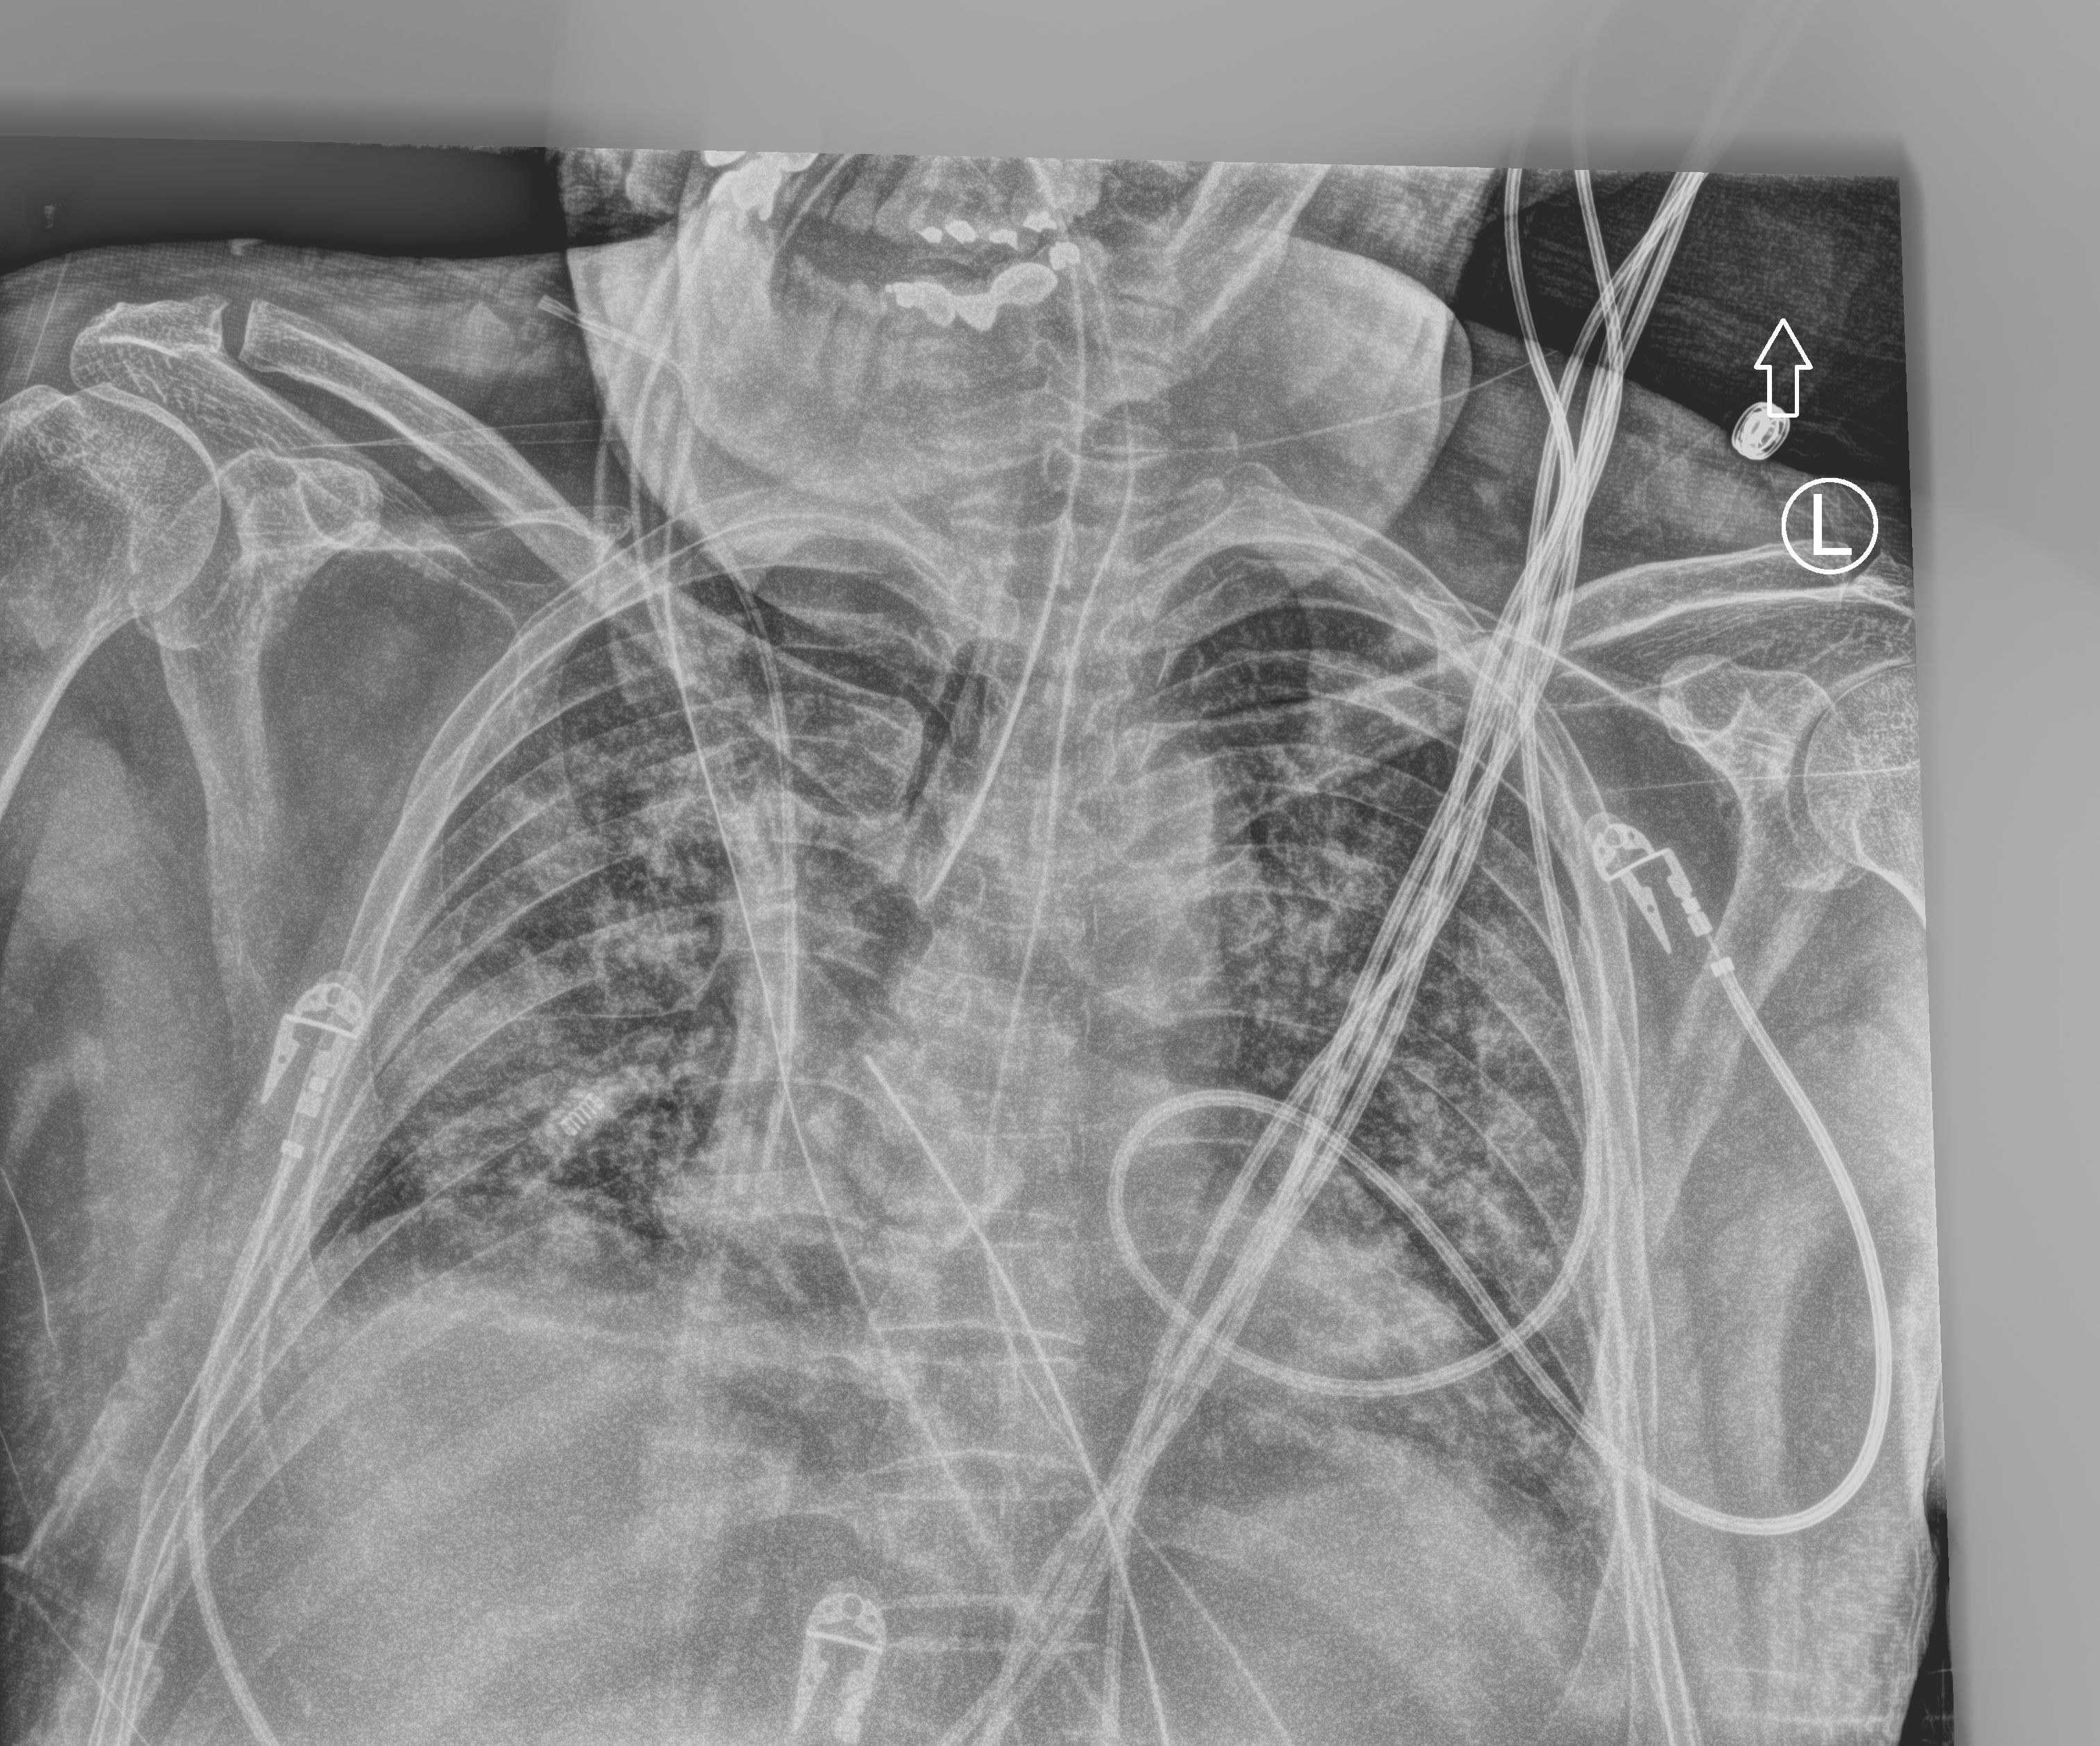
Bedside chest radiograph (computed radiography), anteroposterior (AP) projection. Patient hospitalised with COVID-19; male, aged 60–74 years.
Hospital-stay facts (about this admission, not read from this image; timing relative to this image not recorded): admitted to intensive care during this hospital stay: yes.